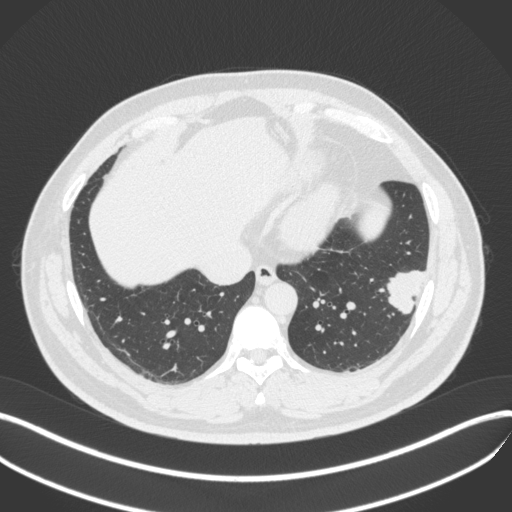
Chest CT, one axial slice; position 128 of 420 along the scan axis; reconstruction kernel B31f; lung window (W 1500 / L -600 HU); 1 mm slice thickness; 512 × 512 image matrix, field of view 400 × 400 mm. Male patient, age 39 years. From the clinical record (not read from this slice): clinical TNM (as recorded): T2a N0 M0; histopathological grade: G2-3.
Annotated regions visible in this slice (rectangle marked by the reading radiologist):
- lung tumour (recorded histology: adenocarcinoma): bounding box [x1, y1, x2, y2] px = [380, 264, 429, 320]